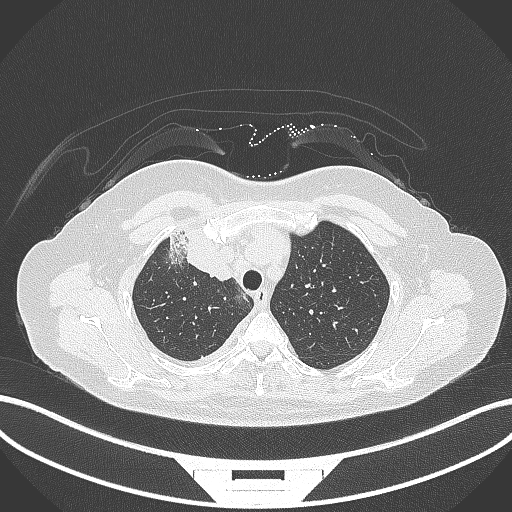
Chest CT, one axial slice. Slice 244 of 305 in the series (ordered by position). Lung window (W 1500 / L -600 HU). 1 mm slice thickness. 512 × 512 image matrix, field of view 400 × 400 mm. Female patient, age 52 years. Case-level facts recorded for this patient, not image findings: clinical TNM (as recorded): T3 N1 M1.
Outlined on this slice (bounding box drawn by a radiologist):
- lung tumour (recorded histology: adenocarcinoma): box from (x=165, y=228) to (x=233, y=283) px